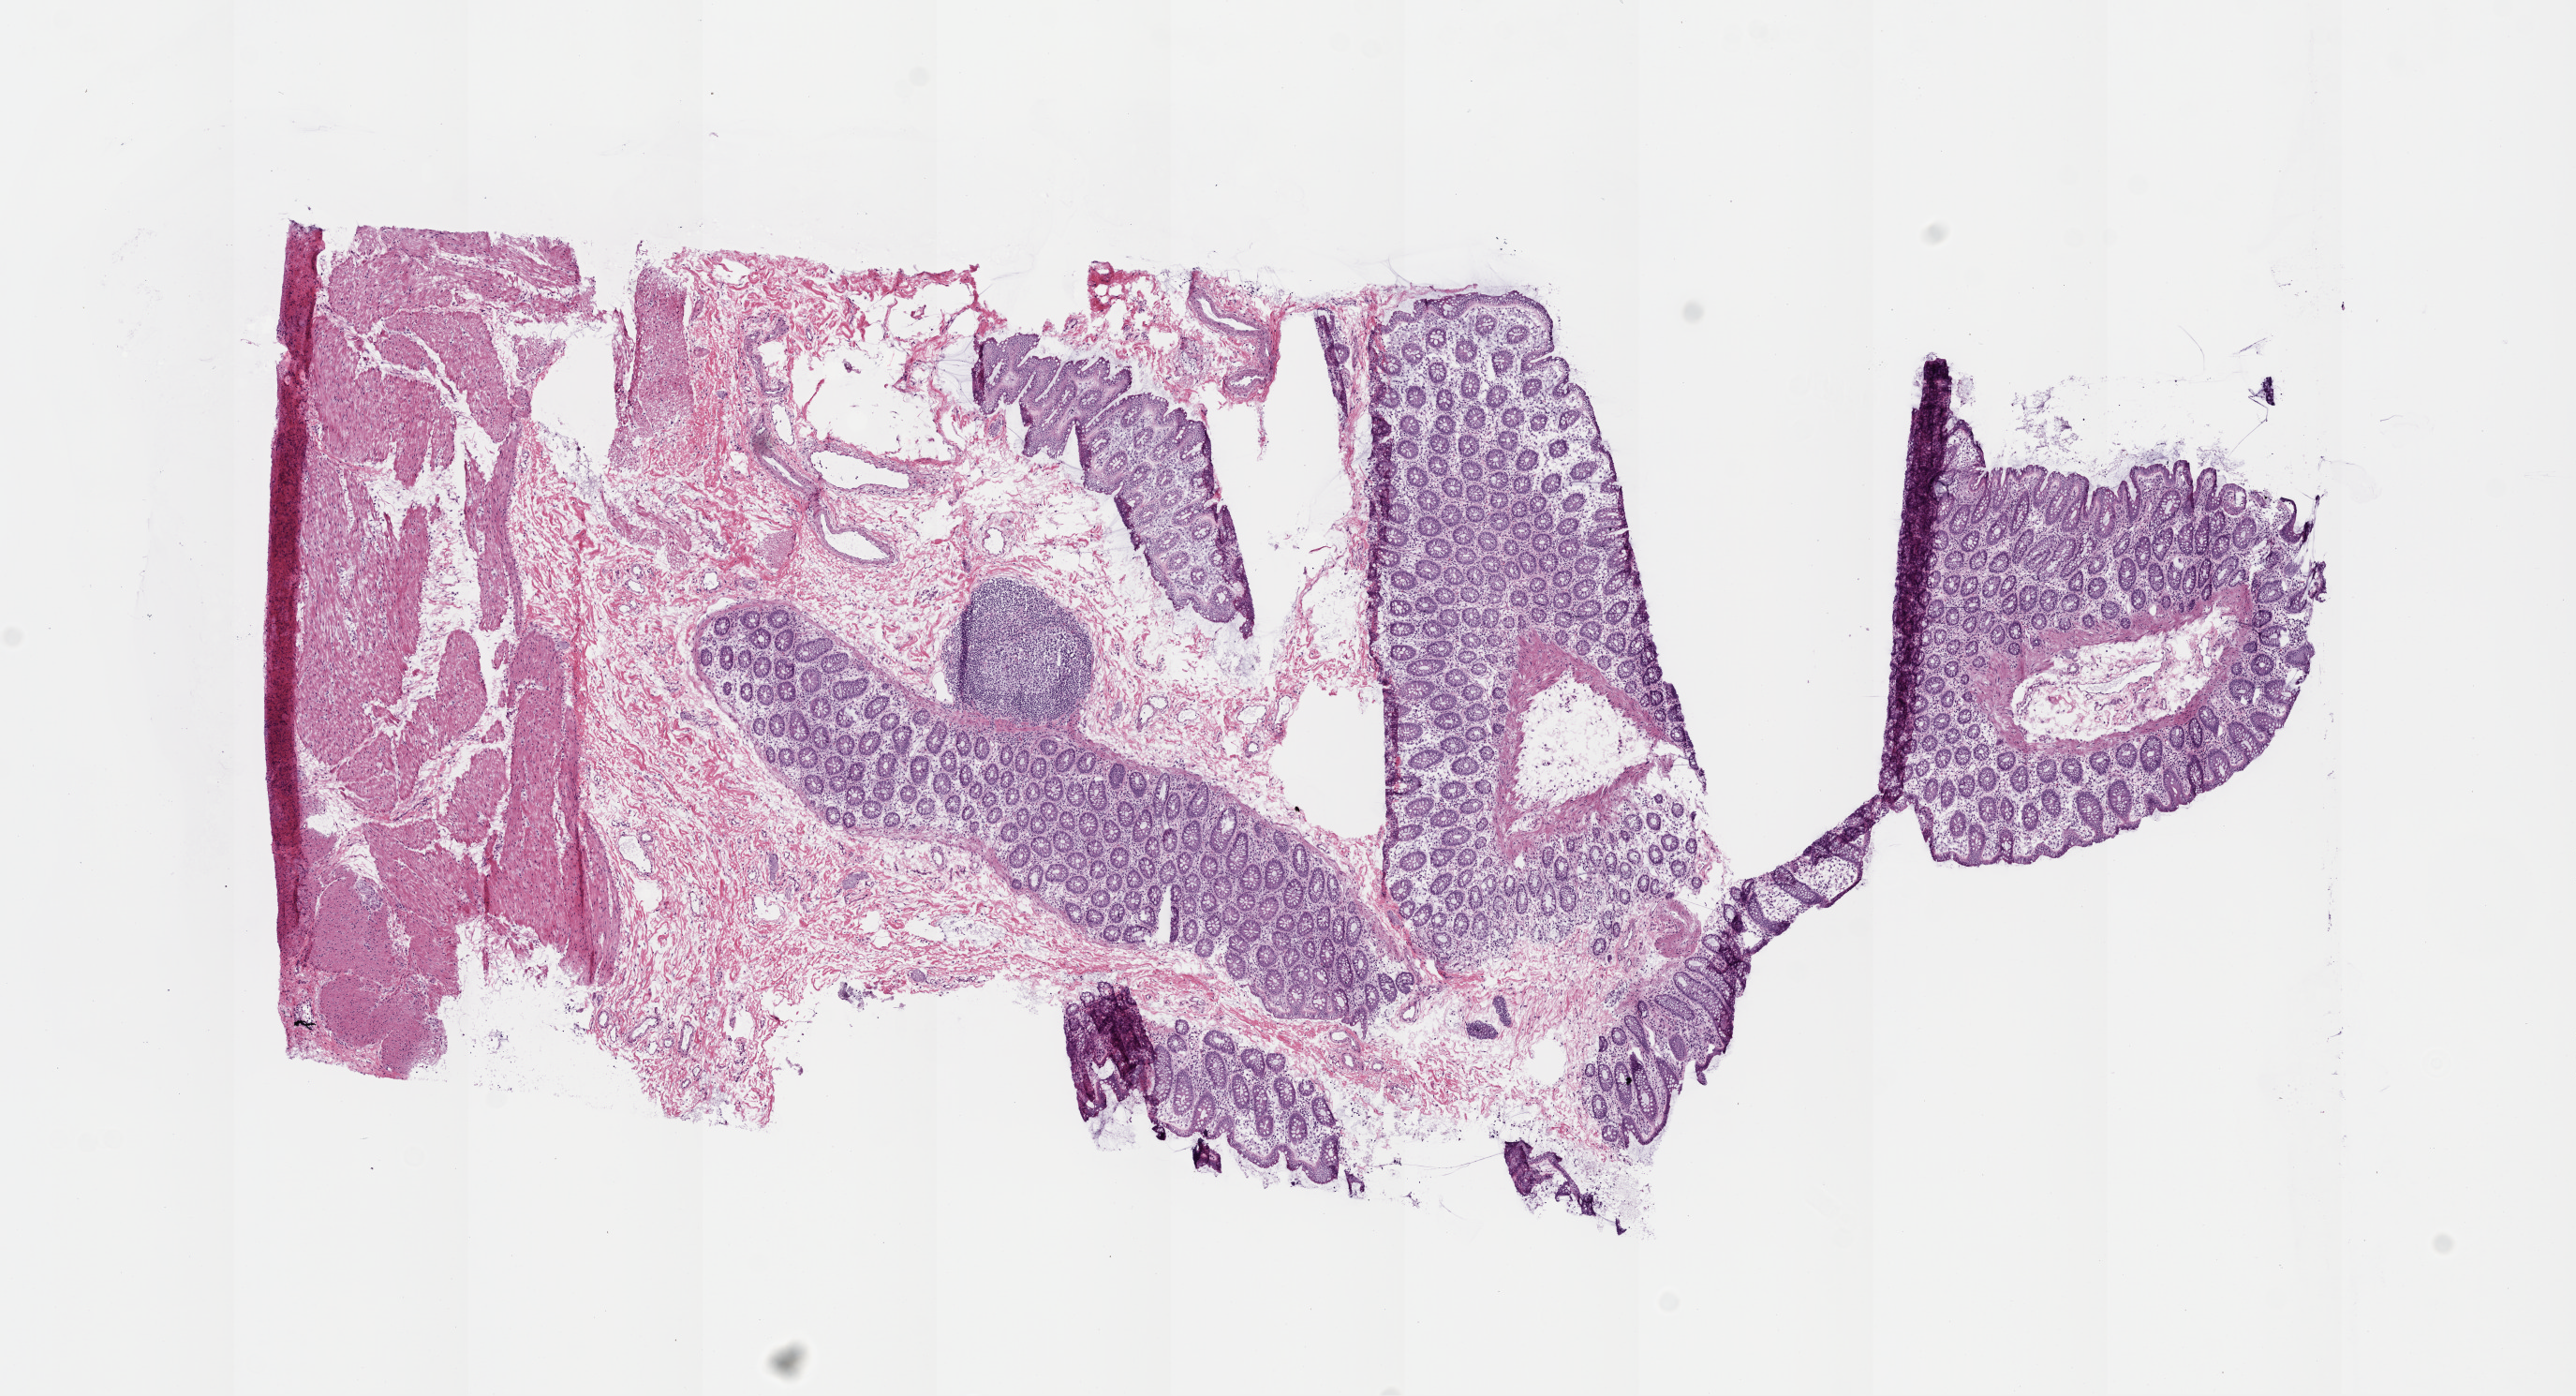
Digitized H&E tissue section (whole slide), a low-resolution overview of the entire scanned area, about 11.0 x 6.0 mm. Frozen section from the top of the tissue portion. Colon, solid tissue normal (non-tumour tissue) sample. Female, age 73 years at initial diagnosis.
This section: solid tissue normal (non-tumour) sample from the same patient. Patient diagnosis: Adenocarcinoma, NOS.